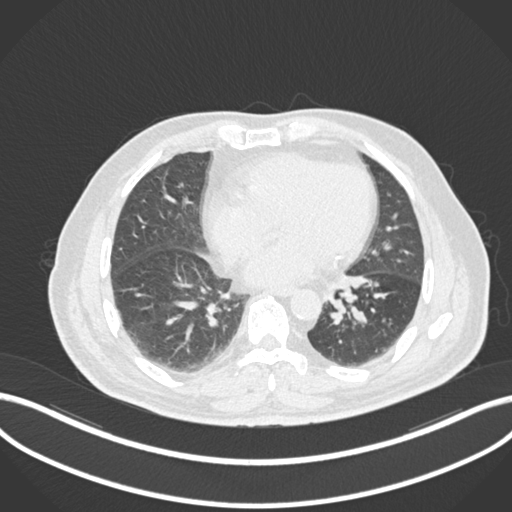
Chest CT, one axial slice; reconstruction kernel B30f; 120 kVp; lung window (W 1500 / L -600 HU); 1 mm slice thickness; 512 × 512 image matrix. Male patient, age 71 years. From the clinical record (not read from this slice): clinical TNM (as recorded): T1b N0 M0.
Structures marked on this image (rectangle marked by the reading radiologist):
- lung tumour (recorded histology: squamous cell carcinoma): bounding box [x1, y1, x2, y2] px = [327, 294, 358, 327]